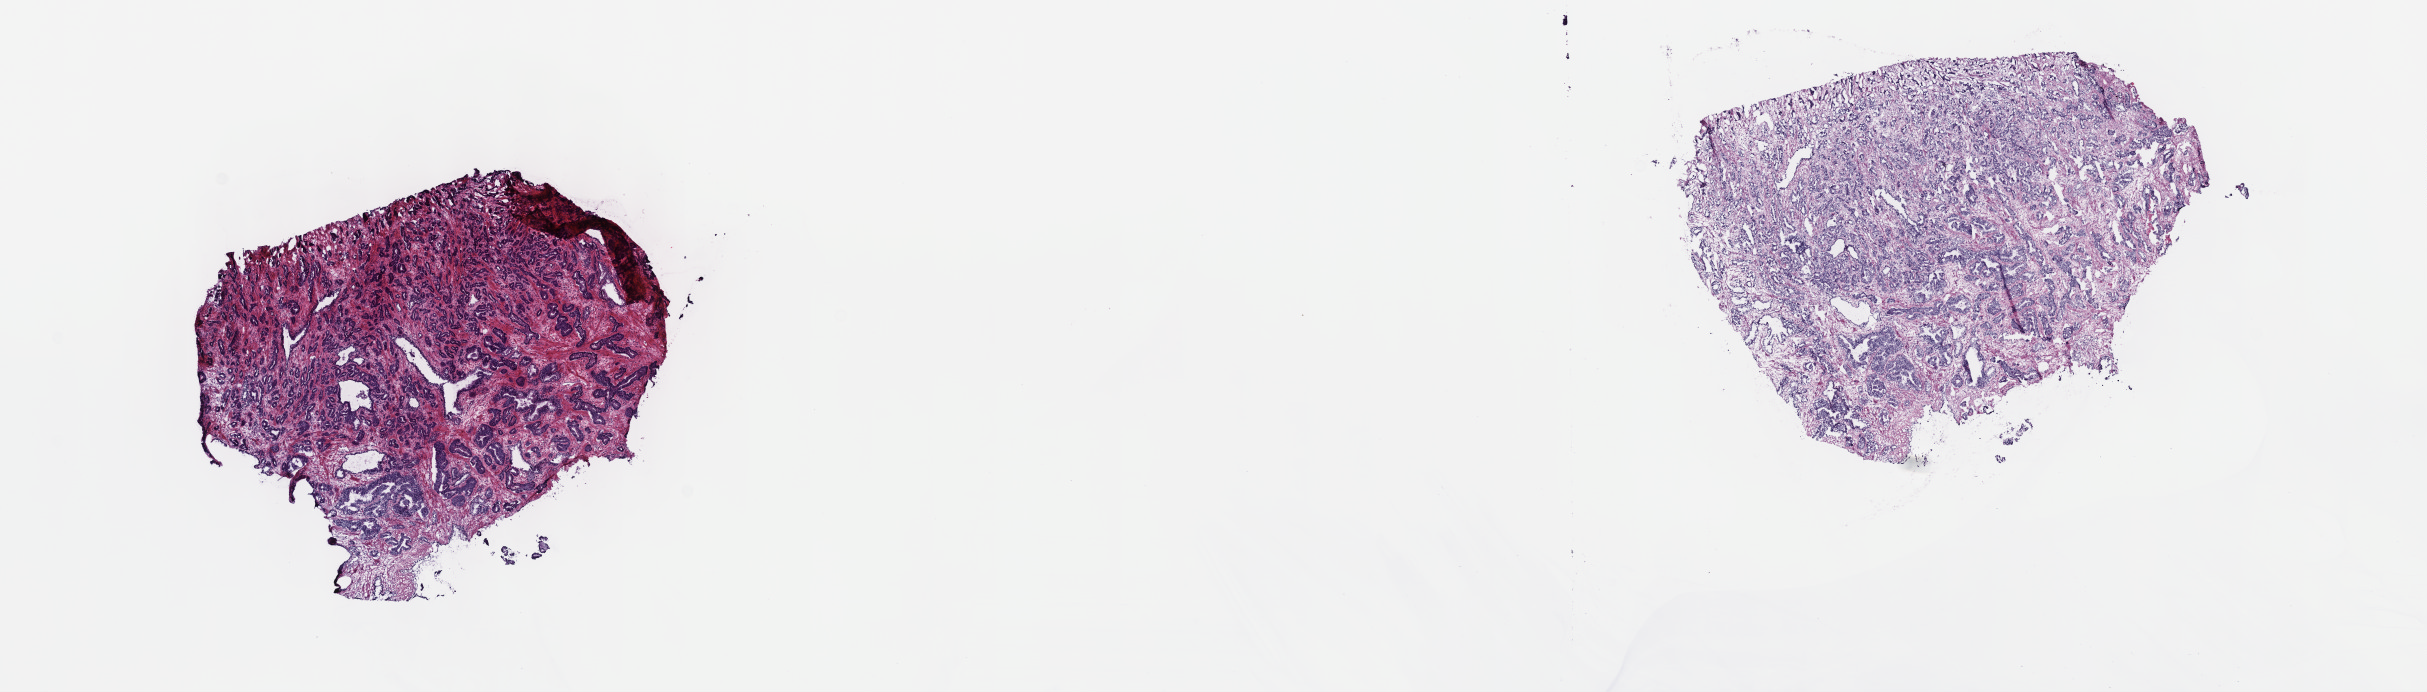
Hematoxylin and eosin (H&E) stained whole-slide image, low-resolution overview of the scanned area, about 19.6 x 5.6 mm, frozen section from the top of the tissue portion, primary tumour sample from the prostate. Male, age 56 years at initial diagnosis. Gleason score: 6 (3+3). Slide review estimates, as recorded: tumour cells 85%, tumour nuclei 70%, normal cells 5%, stromal cells 10%, necrosis 0%. Infiltration values recorded for this section: lymphocyte infiltration 0%, monocyte infiltration 0%, neutrophil infiltration 0%.
* histologic diagnosis: Adenocarcinoma, NOS (prostate gland)
* laterality: bilateral